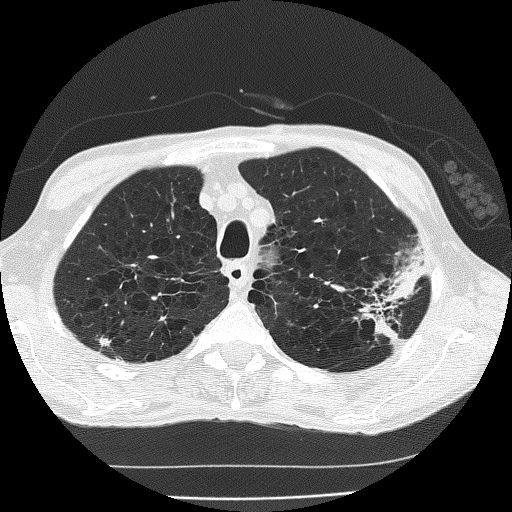
Low-dose screening chest CT, one axial slice; slice 148 of 185 in the series (ordered by position); lung window (W 1500 / L -600 HU); 2 mm slice thickness; 512 × 512 image matrix, field of view 320 × 320 mm.
Structures marked on this image (manually delineated by an expert):
- lesion 1 (tumor, upper lobe of left lung): bounding box (x1, y1, x2, y2) in pixels: (361, 264, 423, 346)